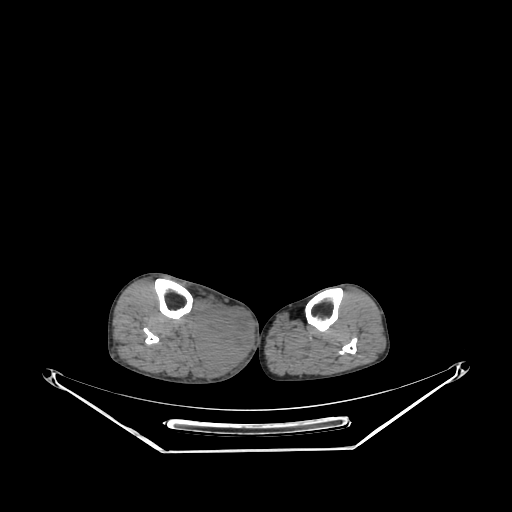
CT of an extremity soft-tissue mass (from a PET/CT study), one axial slice. Position 137 of 267 along the scan axis. 140 kVp. Soft-tissue window (W 400 / L 40 HU). 3.75 mm slice thickness. 512 × 512 image matrix, field of view 500 × 500 mm. Male patient. From the clinical record (not read from this slice): histological type: pleiomorphic liposarcoma; grade: high; site of the primary tumour: right calf.
Structures marked on this image (expert contour drawn on MRI and transferred to this co-registered scan by the dataset authors):
- gross tumour volume including surrounding oedema: bounding box (x1, y1, x2, y2) in pixels: (194, 304, 252, 369)
- gross tumour volume (mass): (194, 306, 252, 366)